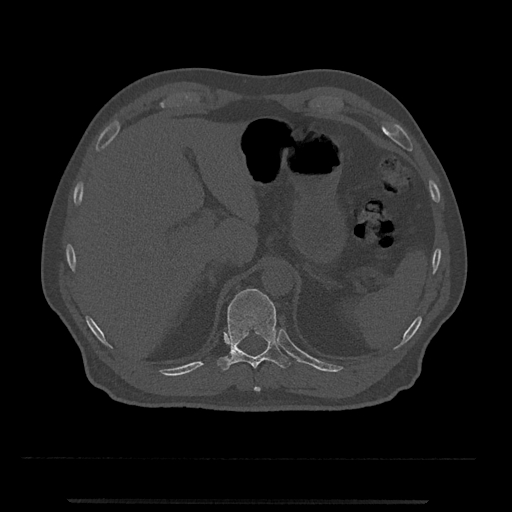
CT including the spine, one axial slice. Slice 468 of 797 in the series (ordered by position). Reconstruction kernel Br40s/3. Bone window (W 1800 / L 400 HU). 0.5 mm slice thickness. 512 × 512 image matrix, field of view 419 × 419 mm. Male patient, age 63 years. Case-level facts recorded for this patient, not image findings: primary cancer: prostate.
Annotated regions visible in this slice (semi-automatic segmentation, software-assisted and operator-edited):
- T10 vertebra: bounding box (x1, y1, x2, y2) in pixels: (254, 387, 261, 392)
- T11 vertebra: (218, 288, 291, 371)